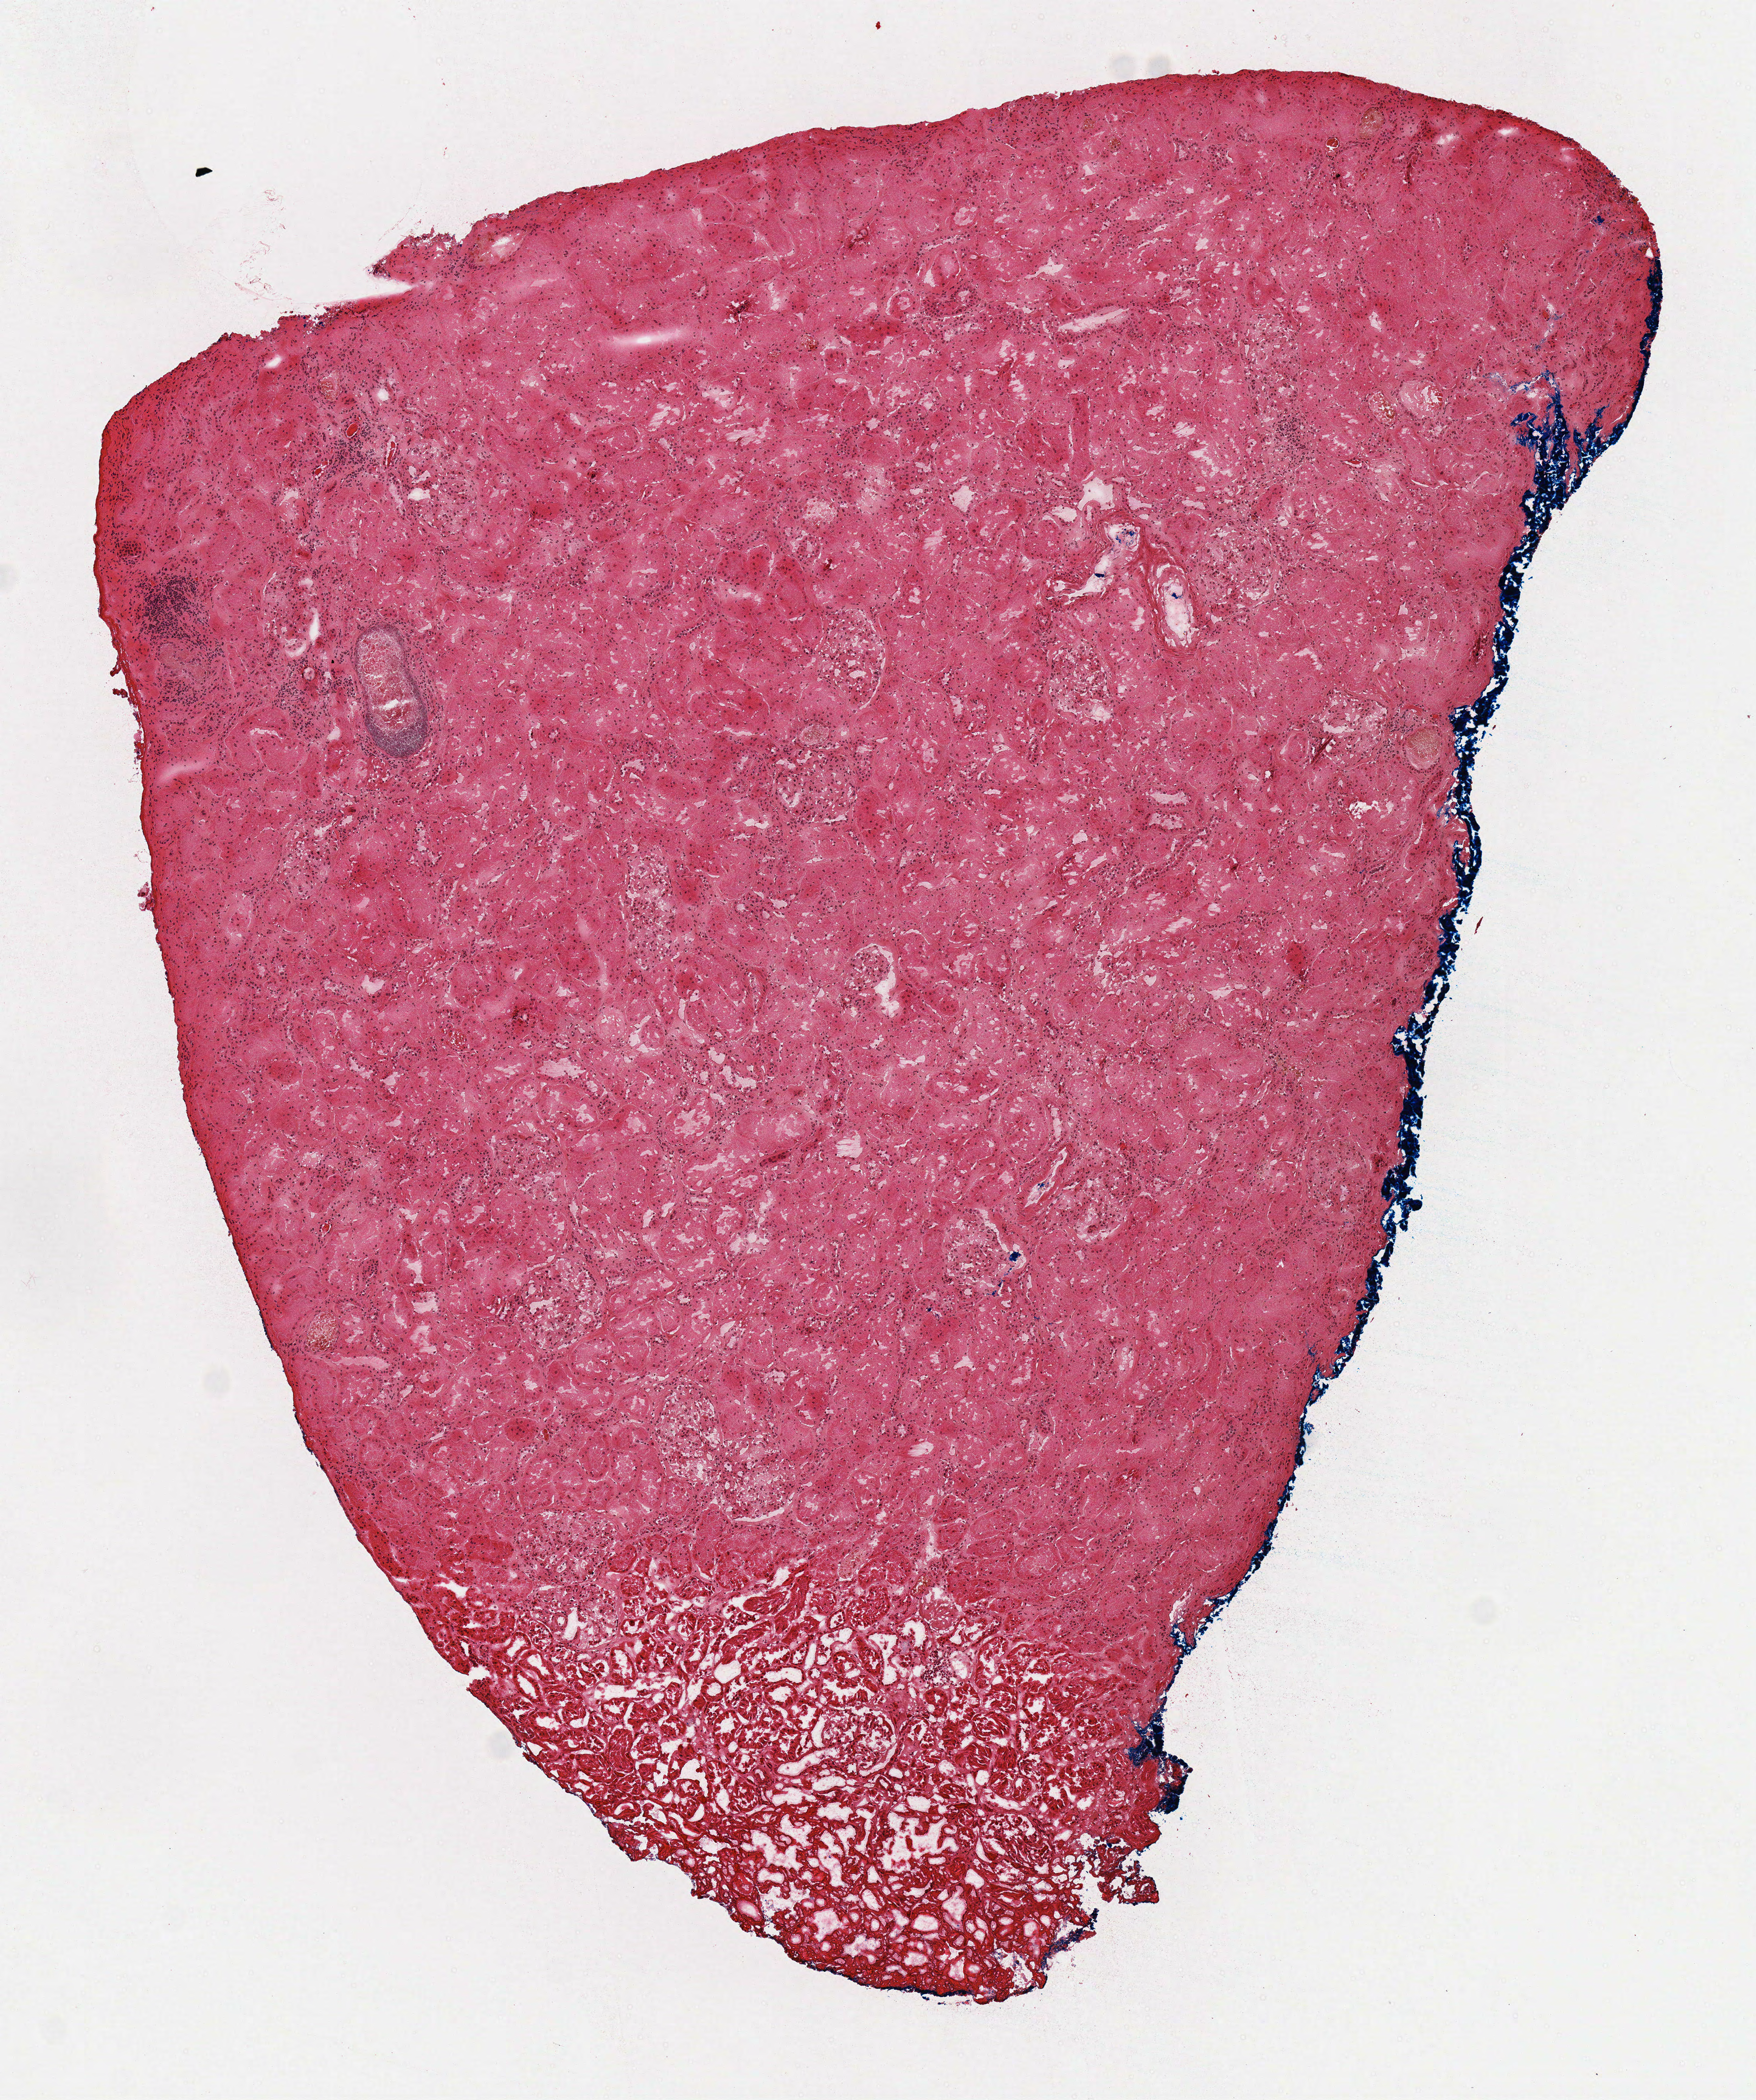
Digitized Hematoxylin and eosin (H&E) stained tissue section (whole slide) — shown as a low-resolution overview of the whole scanned area (about 4.9 x 5.9 mm, slide scanned at 40x). Frozen section from the top of the tissue portion. Solid tissue normal (non-tumour tissue) sample from the kidney. Patient: male, age at initial diagnosis 69 years.
This section: solid tissue normal (non-tumour) sample from the same patient. Patient diagnosis: Papillary adenocarcinoma, NOS.